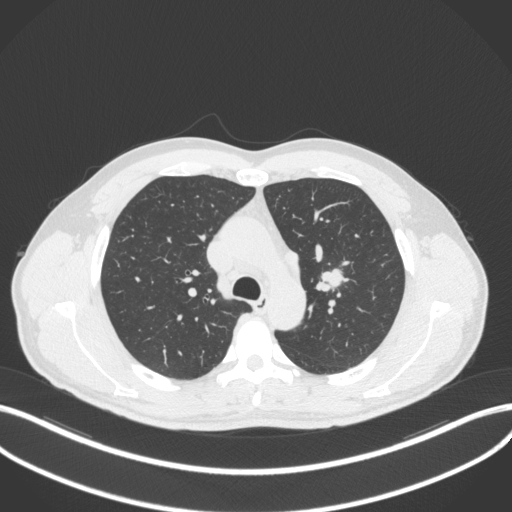
Chest CT, one axial slice. Slice 298 of 383 in the series (ordered by position). 120 kVp. Lung window (W 1500 / L -600 HU). 512 × 512 image matrix, field of view 400 × 400 mm. Male patient, age 50 years. From the clinical record (not read from this slice): clinical TNM (as recorded): T1c N1 M1b.
Annotated regions visible in this slice (rectangle marked by the reading radiologist):
- lung tumour (recorded histology: squamous cell carcinoma): bounding box <316,265,347,296> (left, top, right, bottom; pixels)